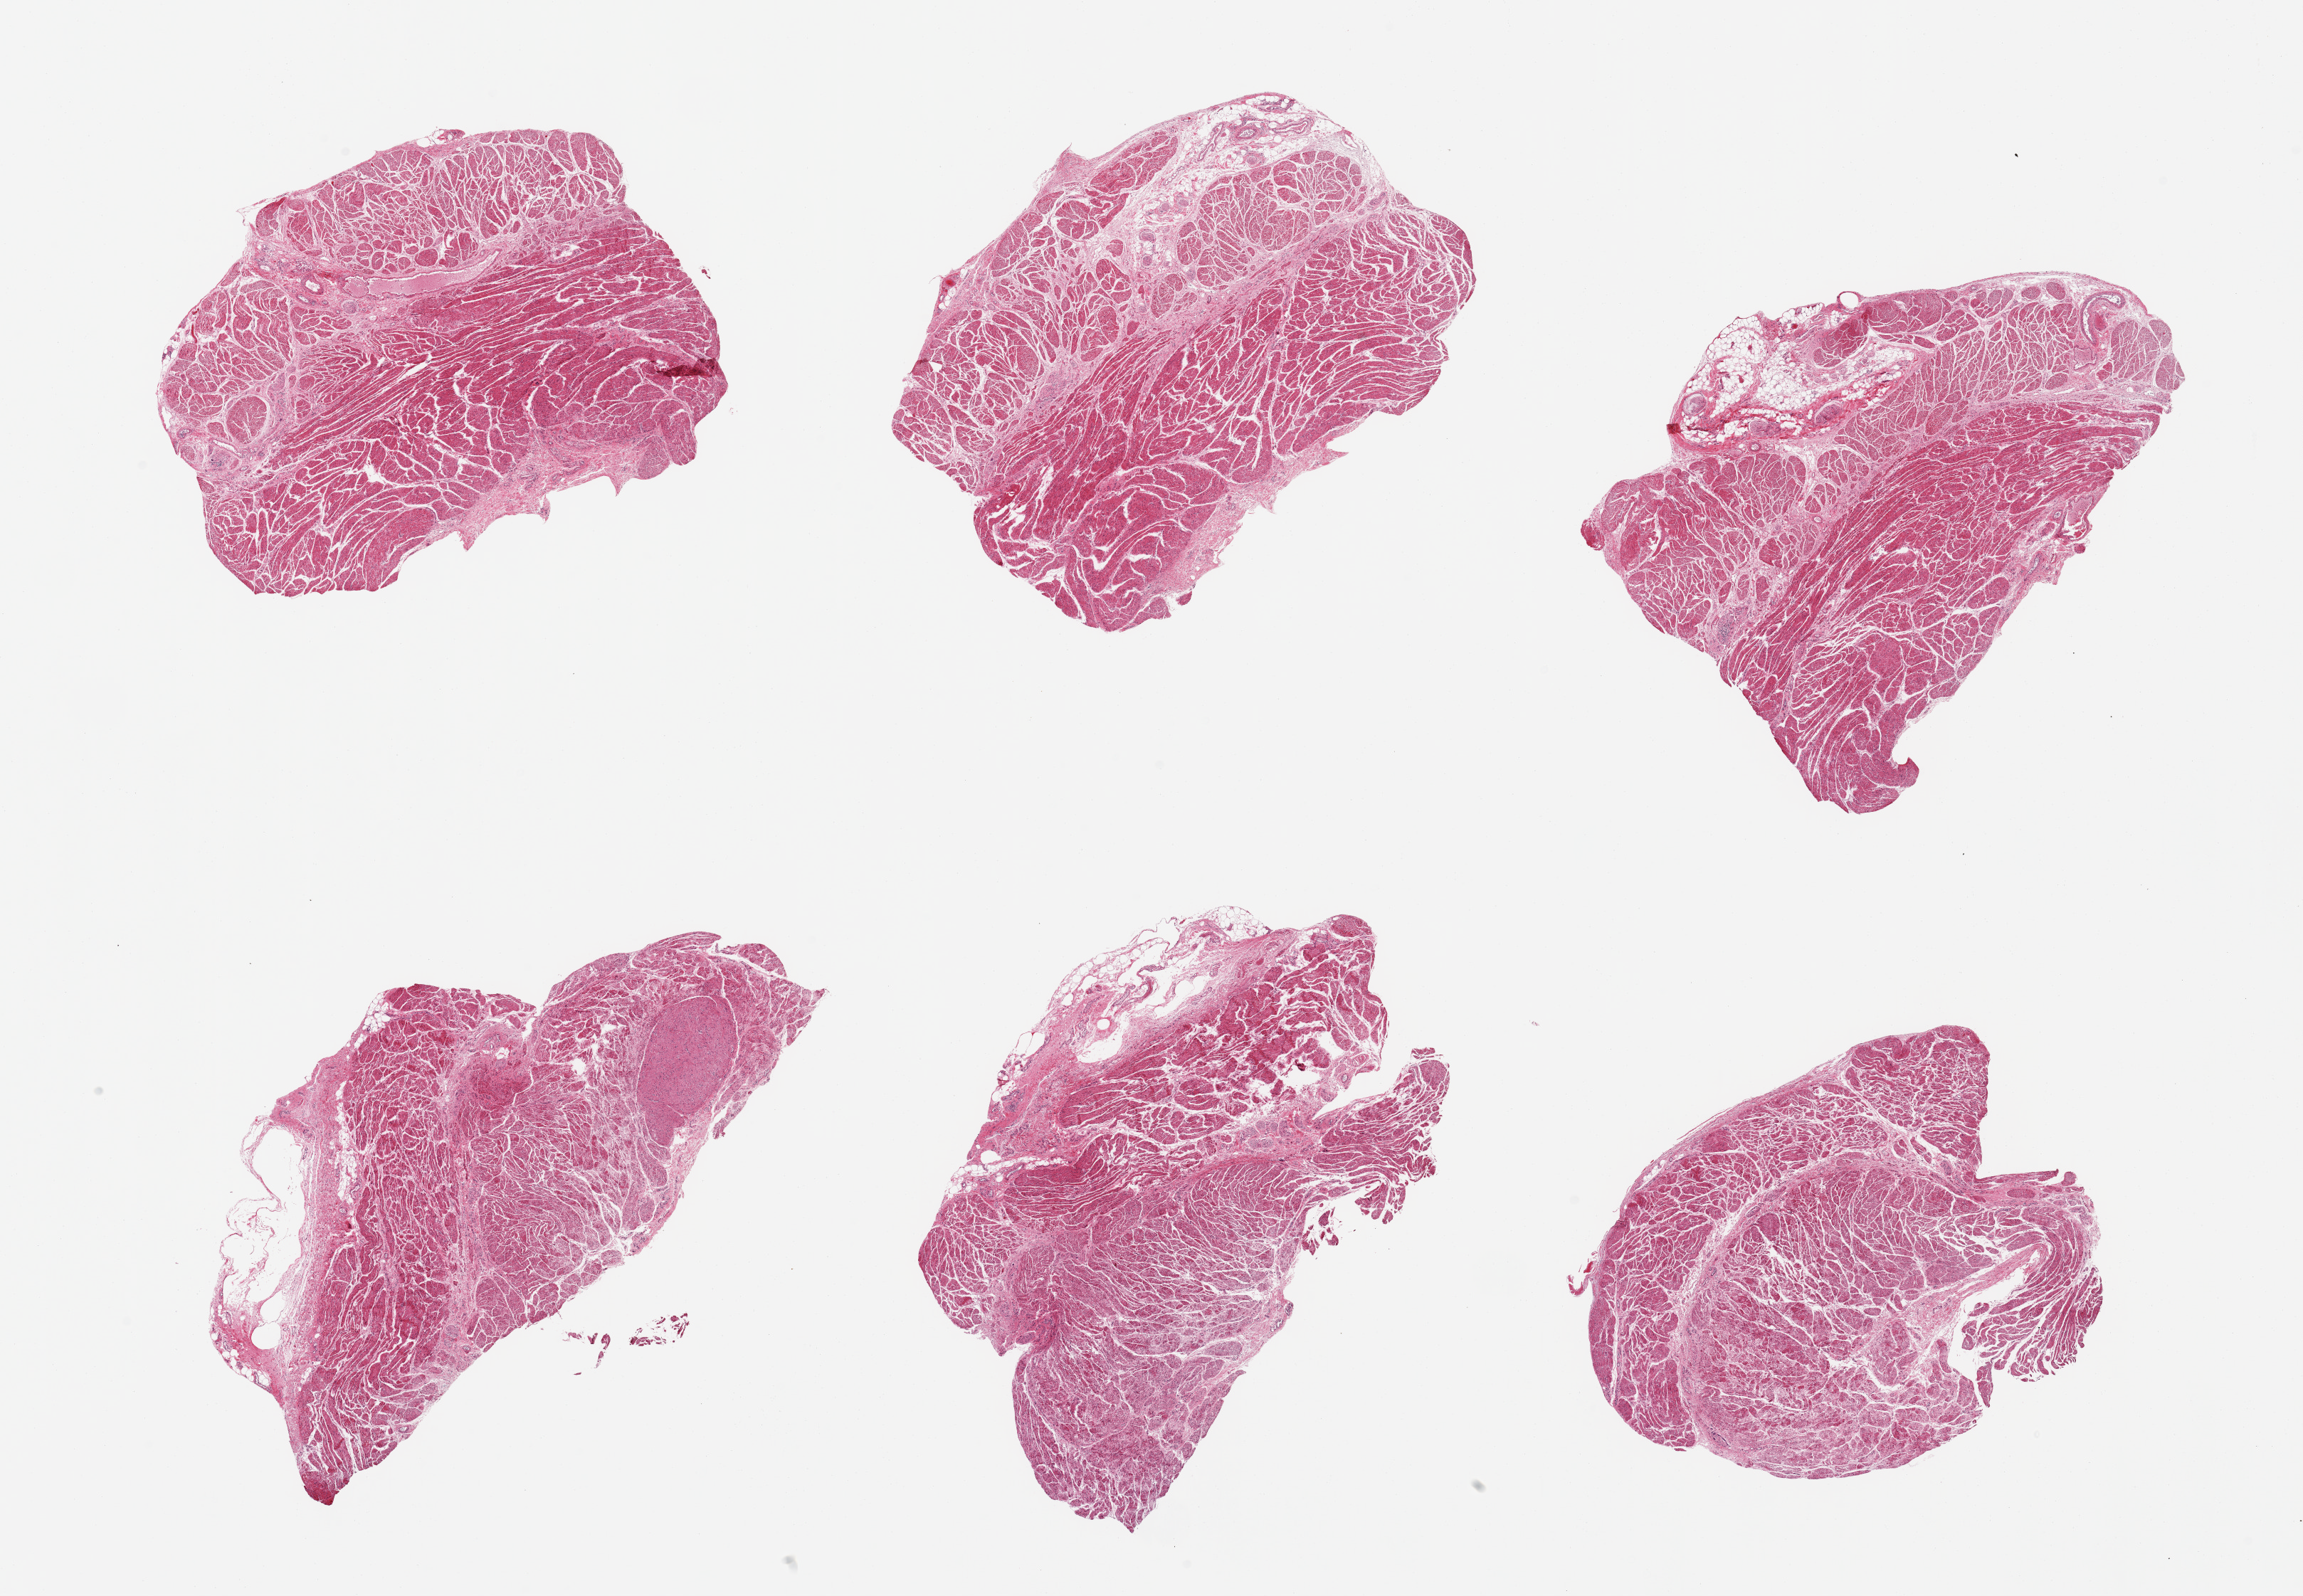
Whole-slide image, hematoxylin and eosin (H&E) stain, brightfield — a low-resolution overview of the entire scanned area, about 25.6 x 17.7 mm, PAXgene-fixed paraffin-embedded (PFPE) section, sampled site (target tissue): gastroesophageal junction, tissue donor sample. Donor sex: male.
Reviewer comment on this tissue sample: 6 pieces, confirmed target muscularis.